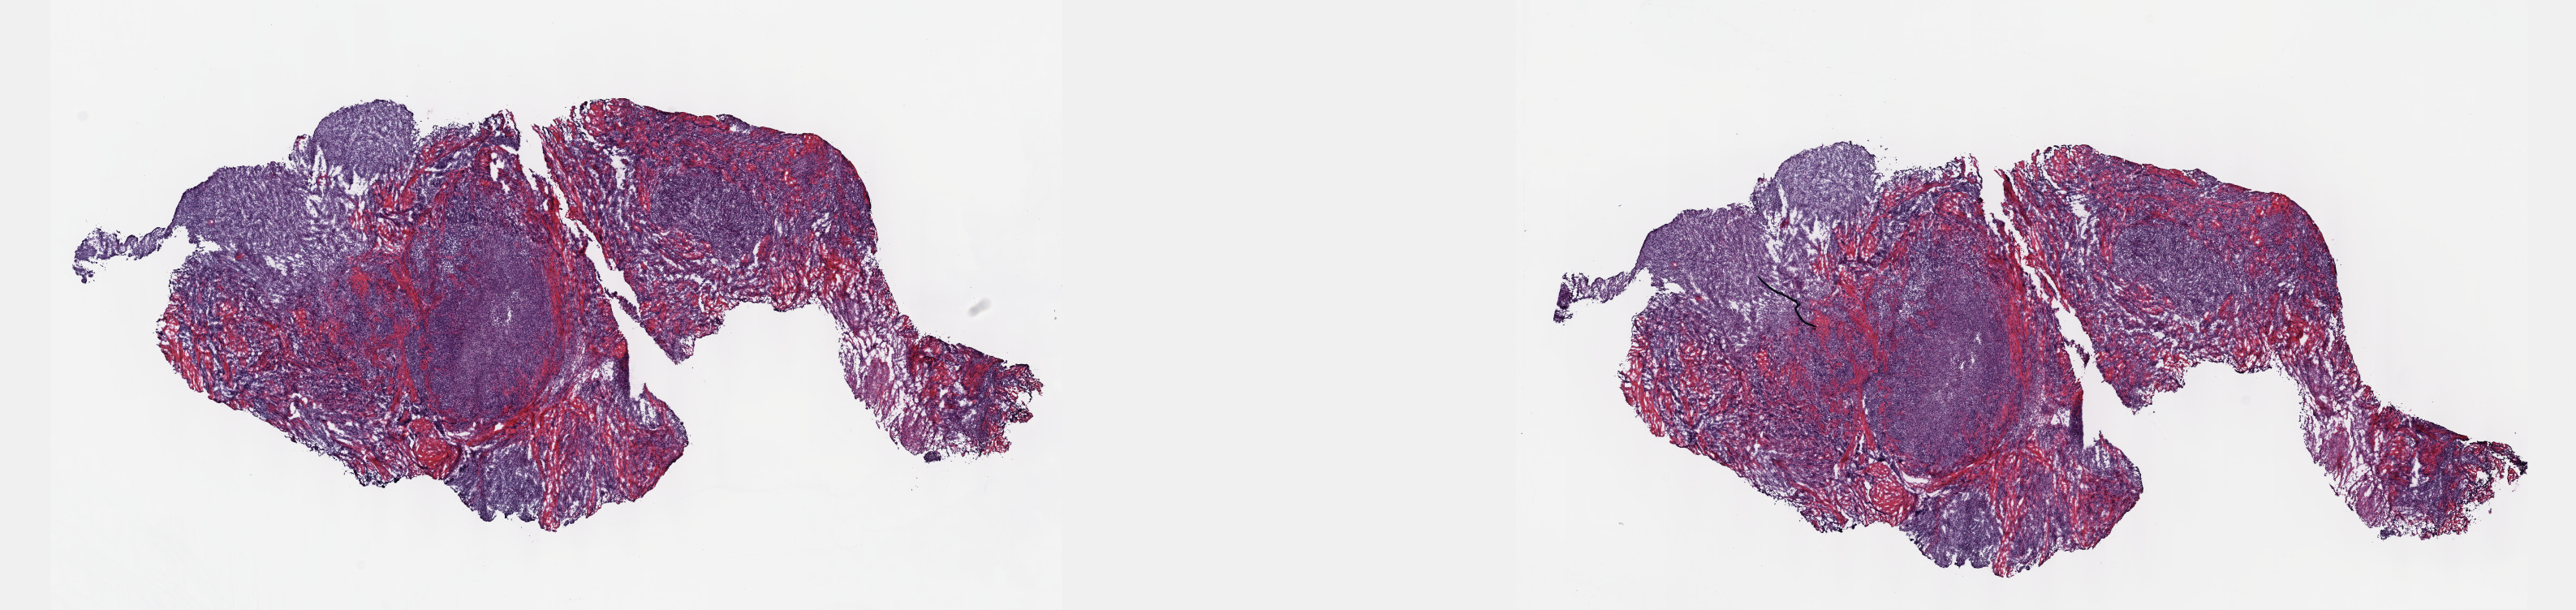
Digitized H&E-stained tissue section (whole slide), a low-resolution overview of the entire scanned area, about 25.7 x 6.1 mm (acquisition: 40x scan). Frozen section from the top of the tissue portion. Sample: primary tumour, thymus. Female patient.
Histologic diagnosis: Thymoma, type AB, malignant.